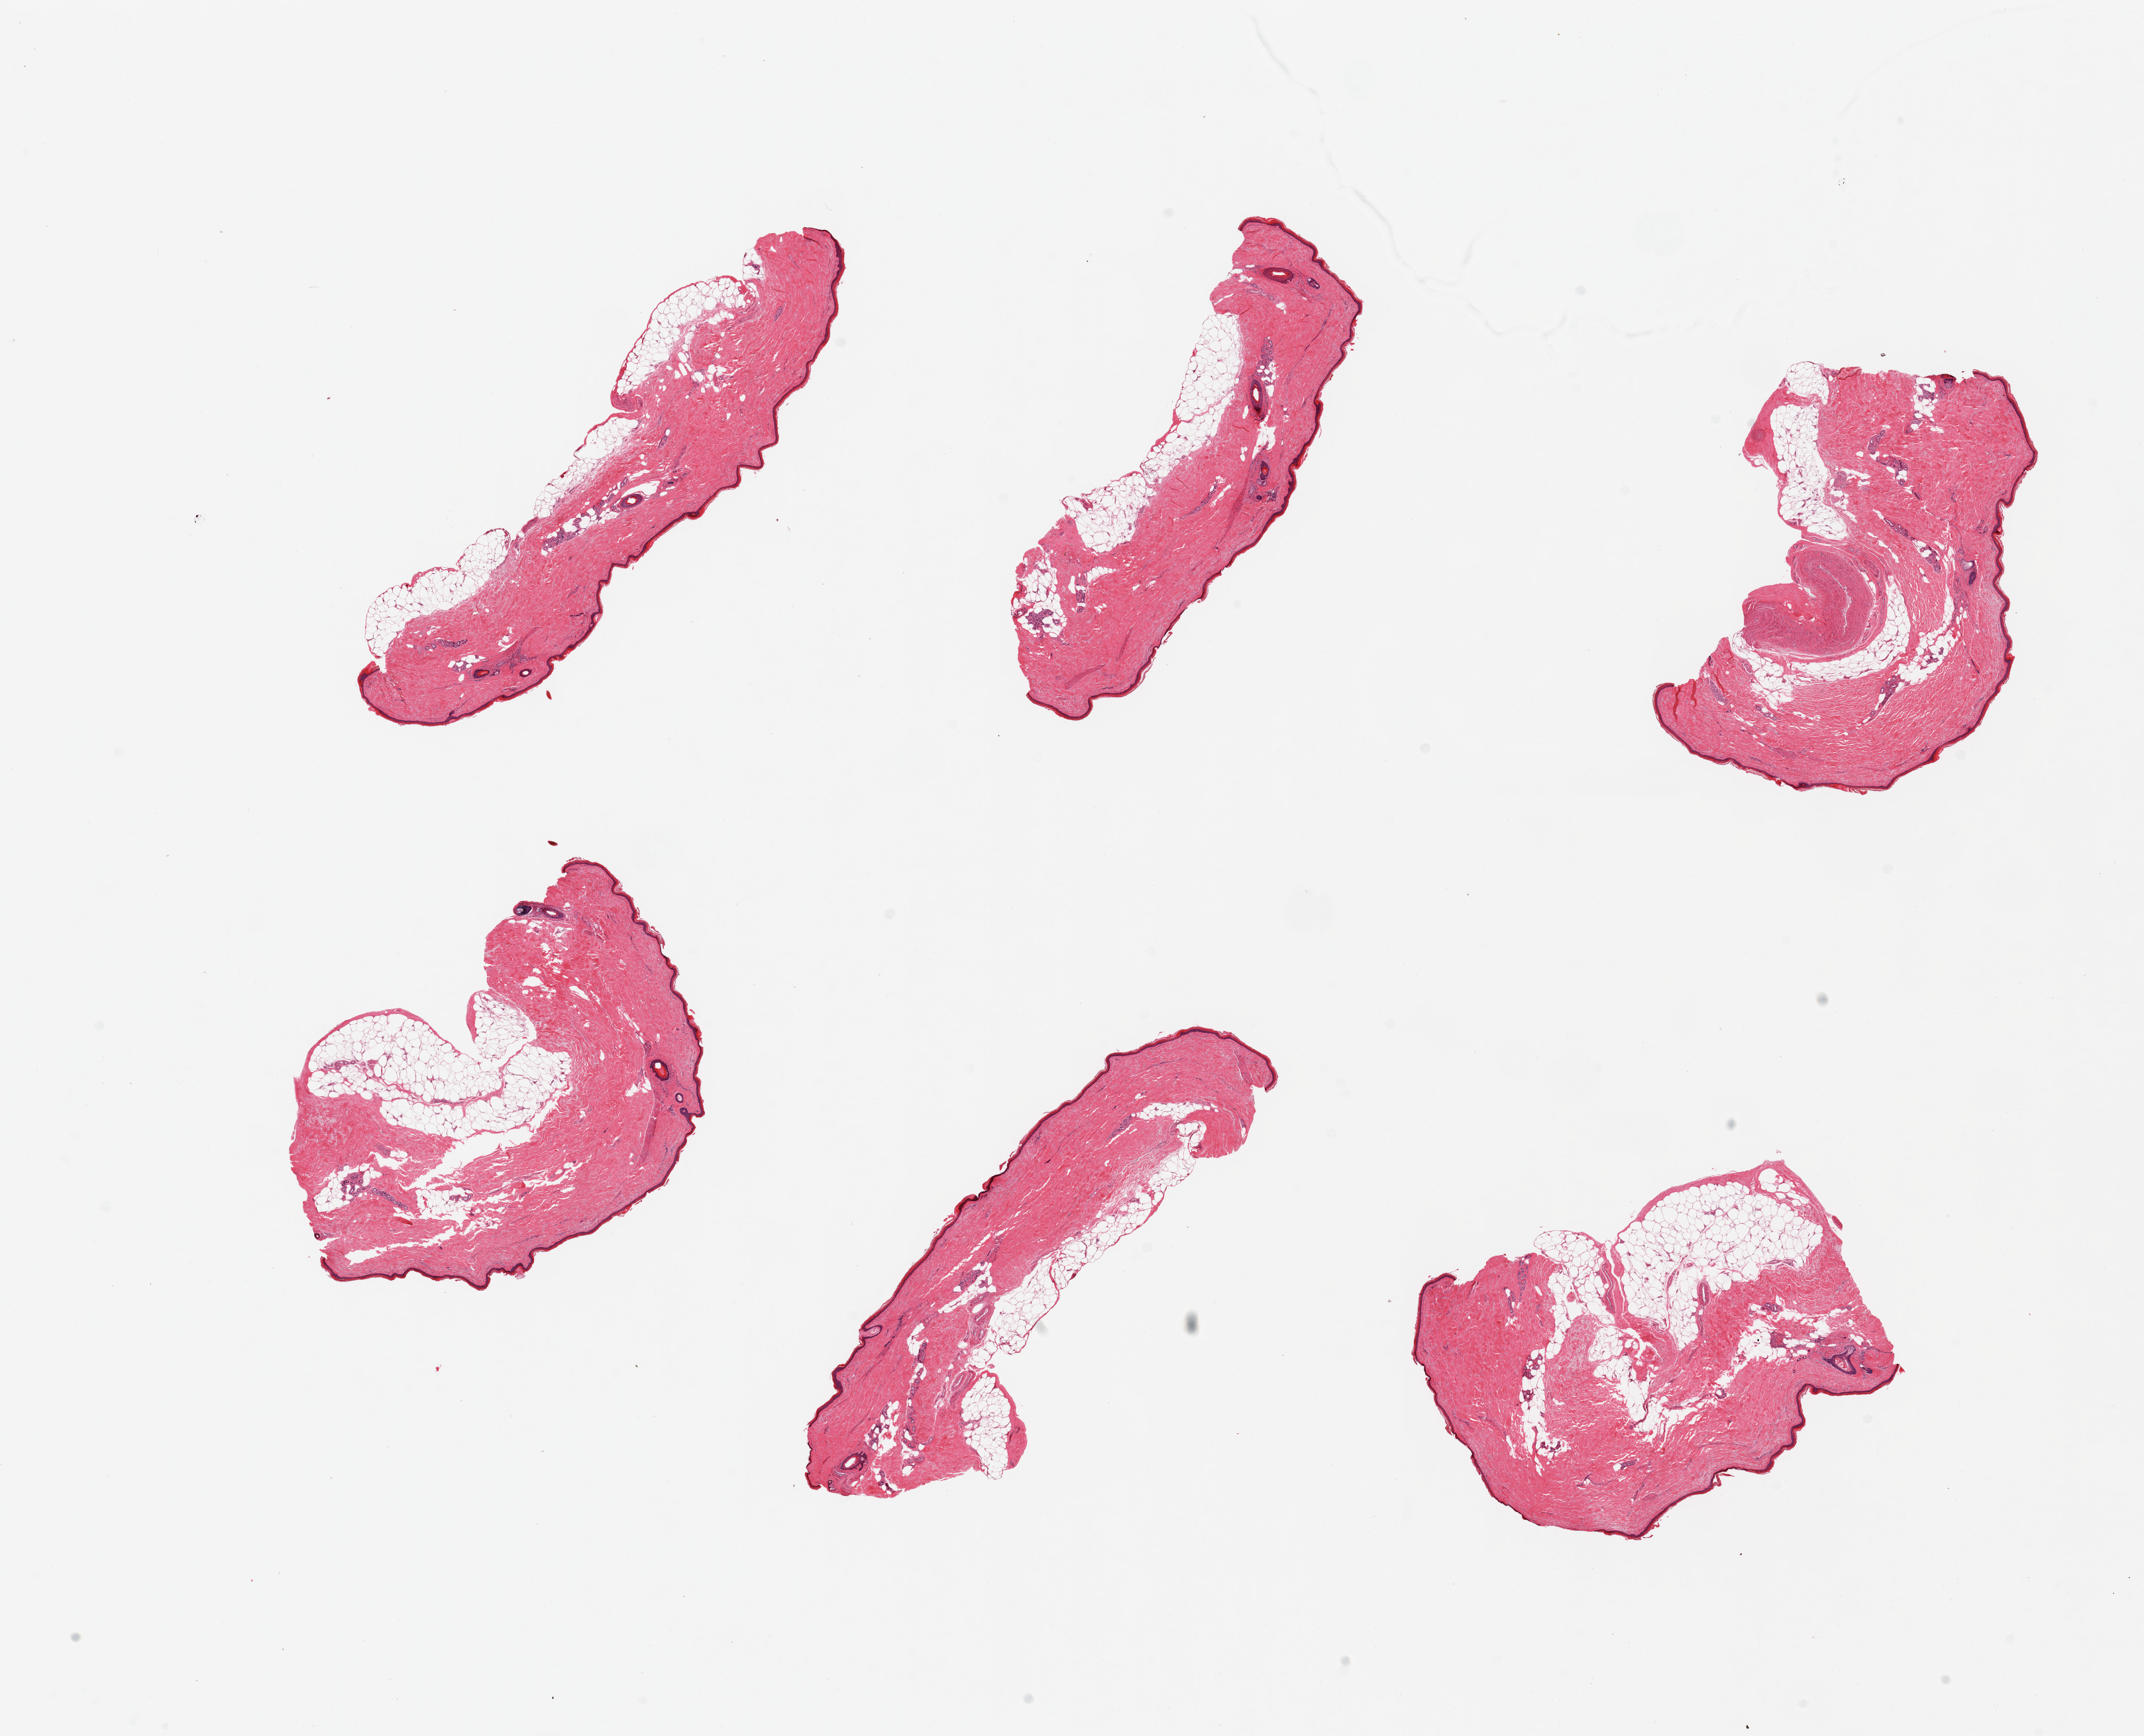
Digitized haematoxylin and eosin-stained section, shown as a low-resolution overview of the whole scanned area (about 25.6 x 20.7 mm, acquisition: 20x scan). PAXgene-fixed, paraffin-embedded tissue. Section of skin of lower leg (target tissue). Tissue donor sample. Donor sex: male.
Reviewer comment on this tissue sample: 6 pieces; 10% to 20% external fat and 10% internal fat; 24um thick epidermis; thick walled vessel.